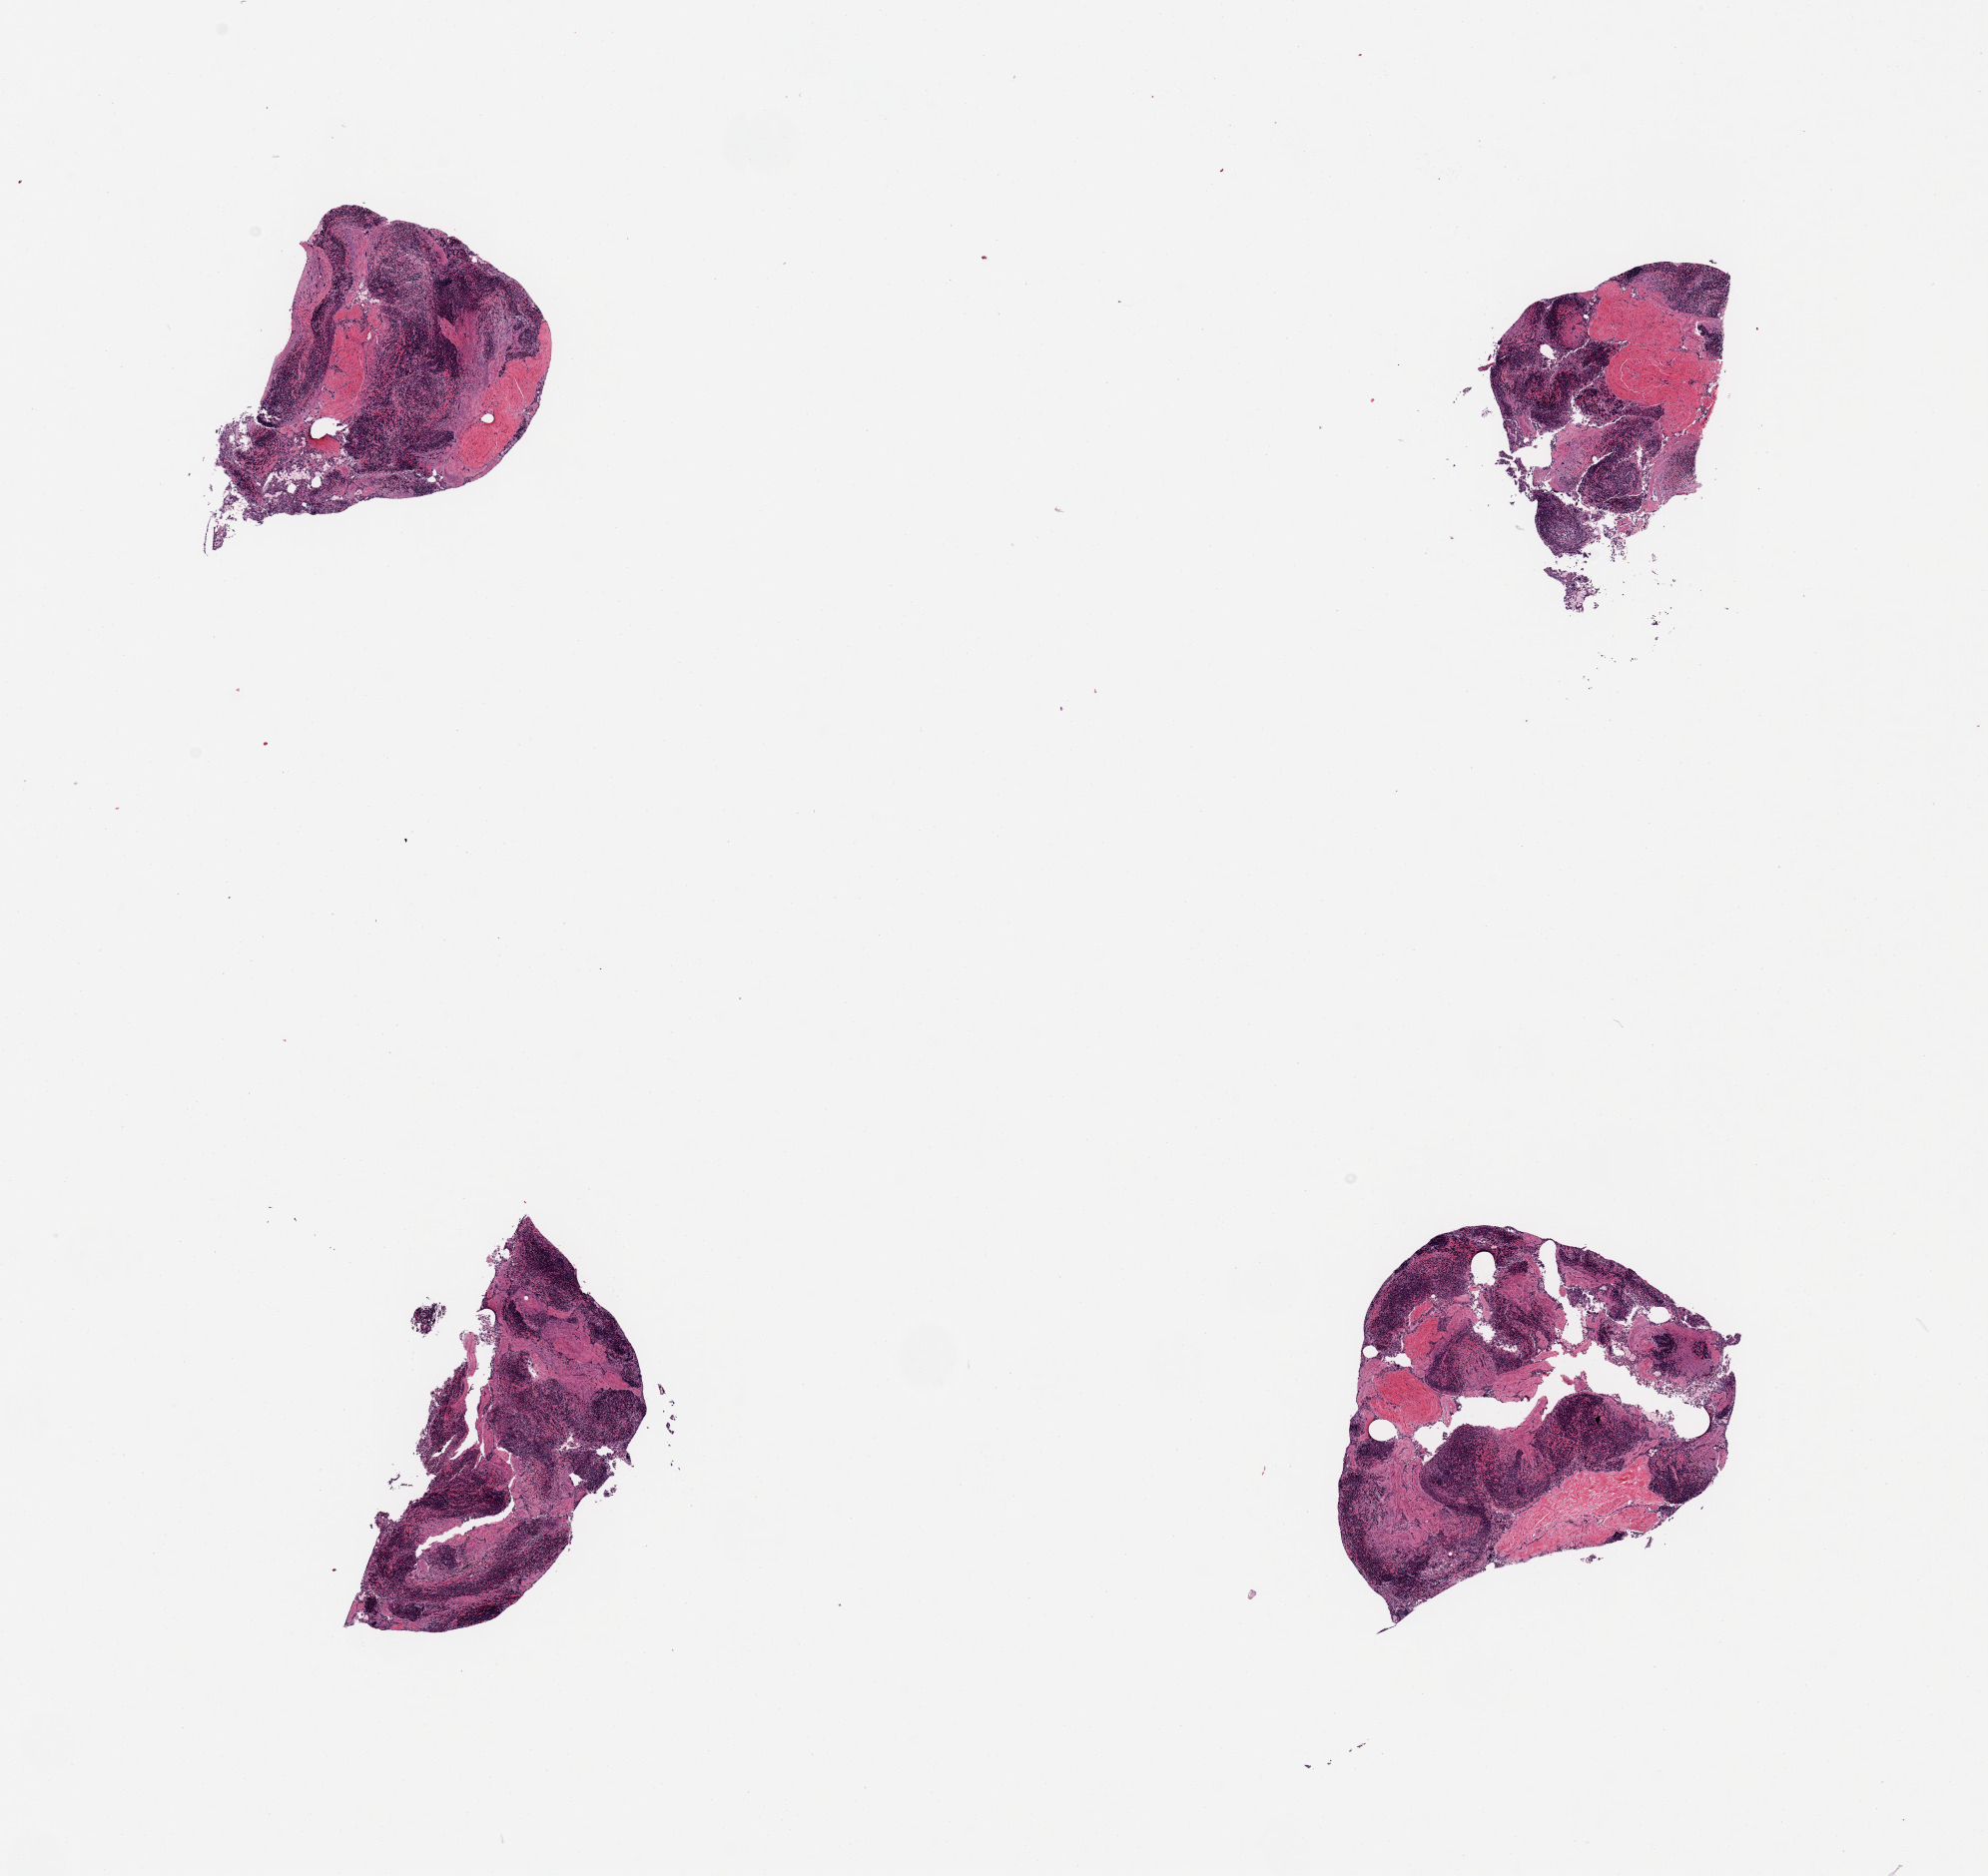
Digitized haematoxylin and eosin-stained section, low-resolution overview of the scanned area, about 15.8 x 14.9 mm. PAXgene-fixed paraffin-embedded (PFPE) section. Sampled site (target tissue): ileum. Tissue donor sample. Donor sex: male.
Reviewer comment on this tissue sample: 4 pieces; autolyzed mucosa and residual target lymphoid aggregates of ~ 50% of tissue, includes residual muscularis (not target).